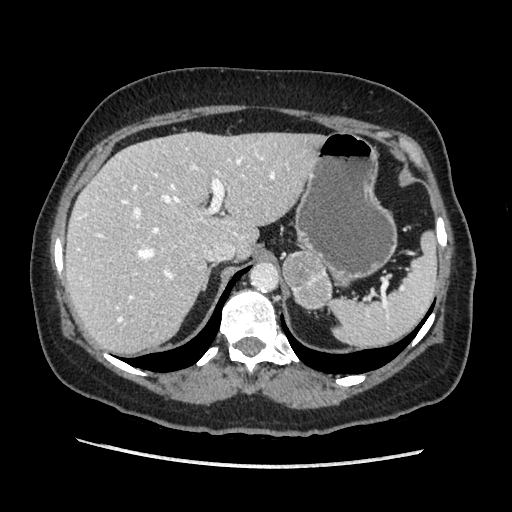
Contrast-enhanced abdominal CT, one axial slice; slice 141 of 203 in the series (ordered by position); soft-tissue window (W 400 / L 40 HU); 1.25 mm slice thickness; 512 × 512 image matrix. Female patient. Case-level facts recorded for this patient, not image findings: diagnosis: adrenocortical carcinoma; tumour side: left adrenal; tumour size at pathology: 6.5 cm.
Structures marked on this image (semi-automatically segmented with operator editing):
- mass: box from (x=282, y=252) to (x=331, y=307) px